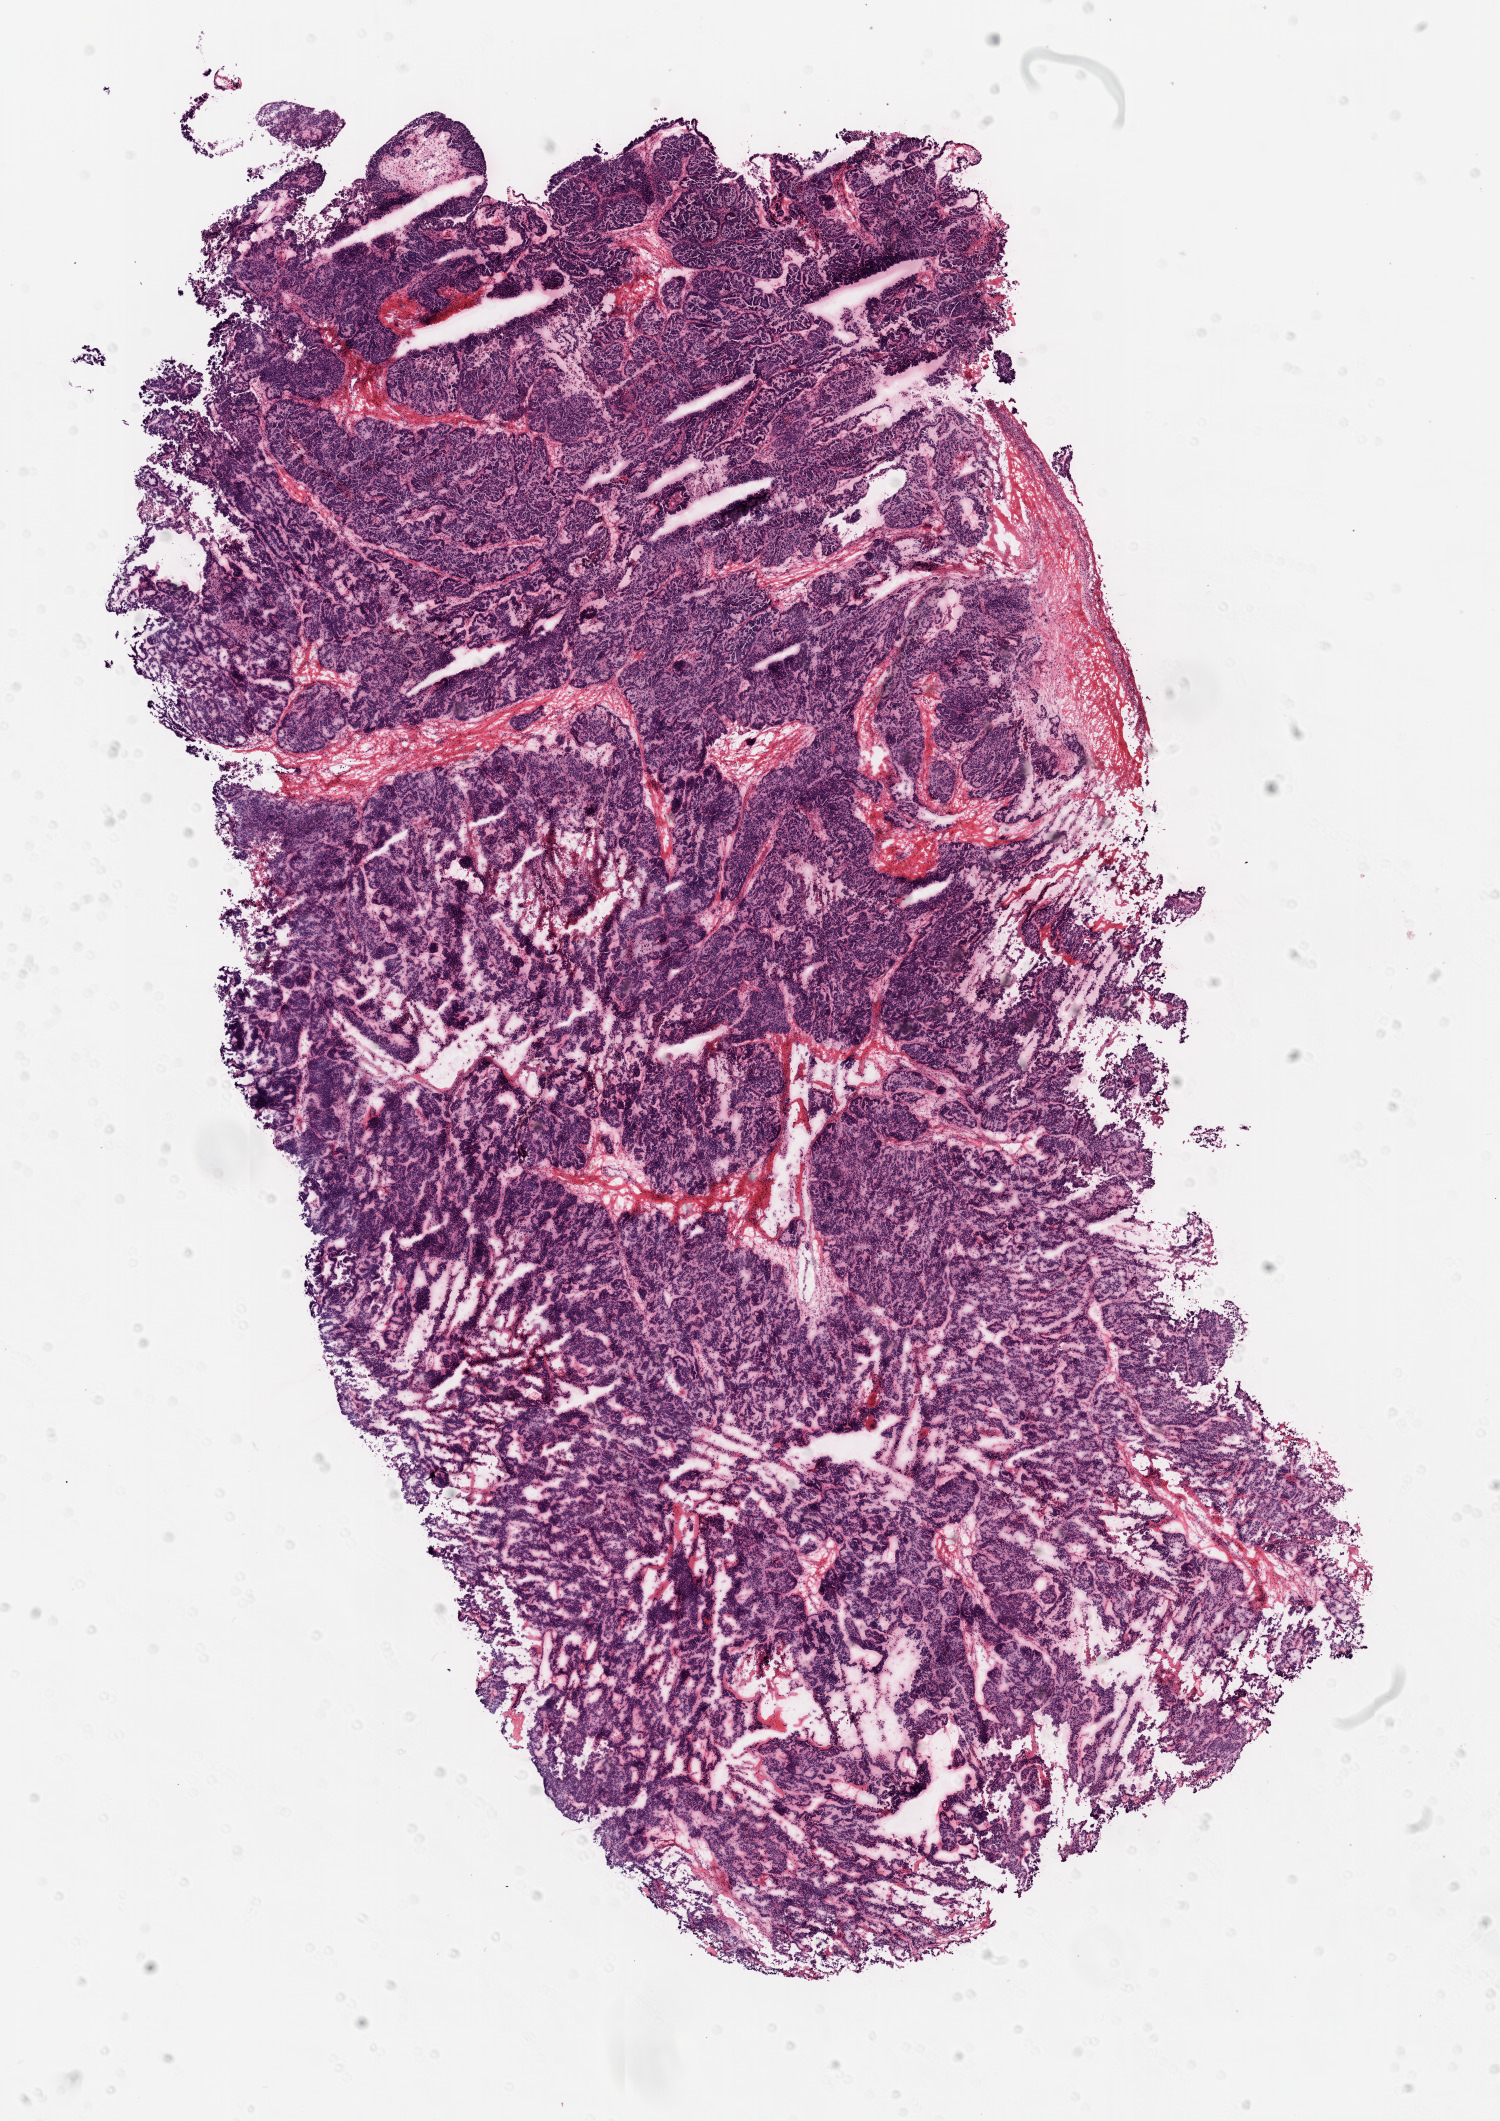
H&E-stained whole-slide image, shown as a low-resolution overview of the whole scanned area (about 12.0 x 17.0 mm, slide scanned at 20x). Frozen section from the top of the tissue portion. Ovary, primary tumour sample. Female patient; age at initial diagnosis 45 years. Histologic grade: G3 (poorly differentiated). Composition of this section per pathologist review: tumour cells 98%, tumour nuclei 99%, normal cells 0%, stromal cells 1%, necrosis 1%.
Pathologic diagnosis: Serous cystadenocarcinoma, NOS. FIGO stage: IIIC. Laterality: bilateral.